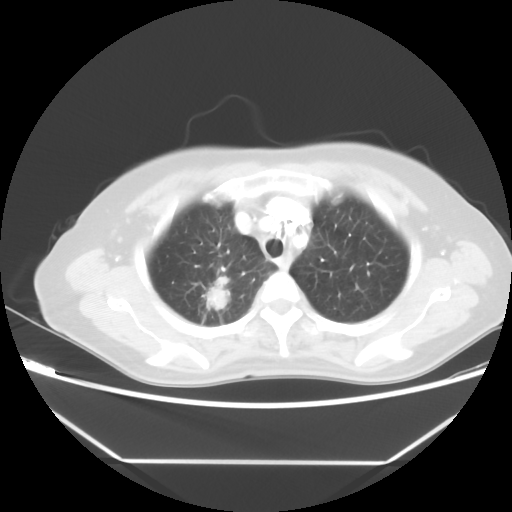
Chest CT, one axial slice. Slice 40 of 48 in the series (ordered by position). Reconstruction kernel STANDARD. 100 kVp. Lung window (W 1500 / L -600 HU). 512 × 512 image matrix, field of view 360 × 360 mm. Female patient, age 65 years. From the clinical record (not read from this slice): clinical TNM (as recorded): T1c N1 M1.
Outlined on this slice (rectangle marked by the reading radiologist):
- lung tumour (recorded histology: adenocarcinoma): bounding box <201,272,235,318> (left, top, right, bottom; pixels)